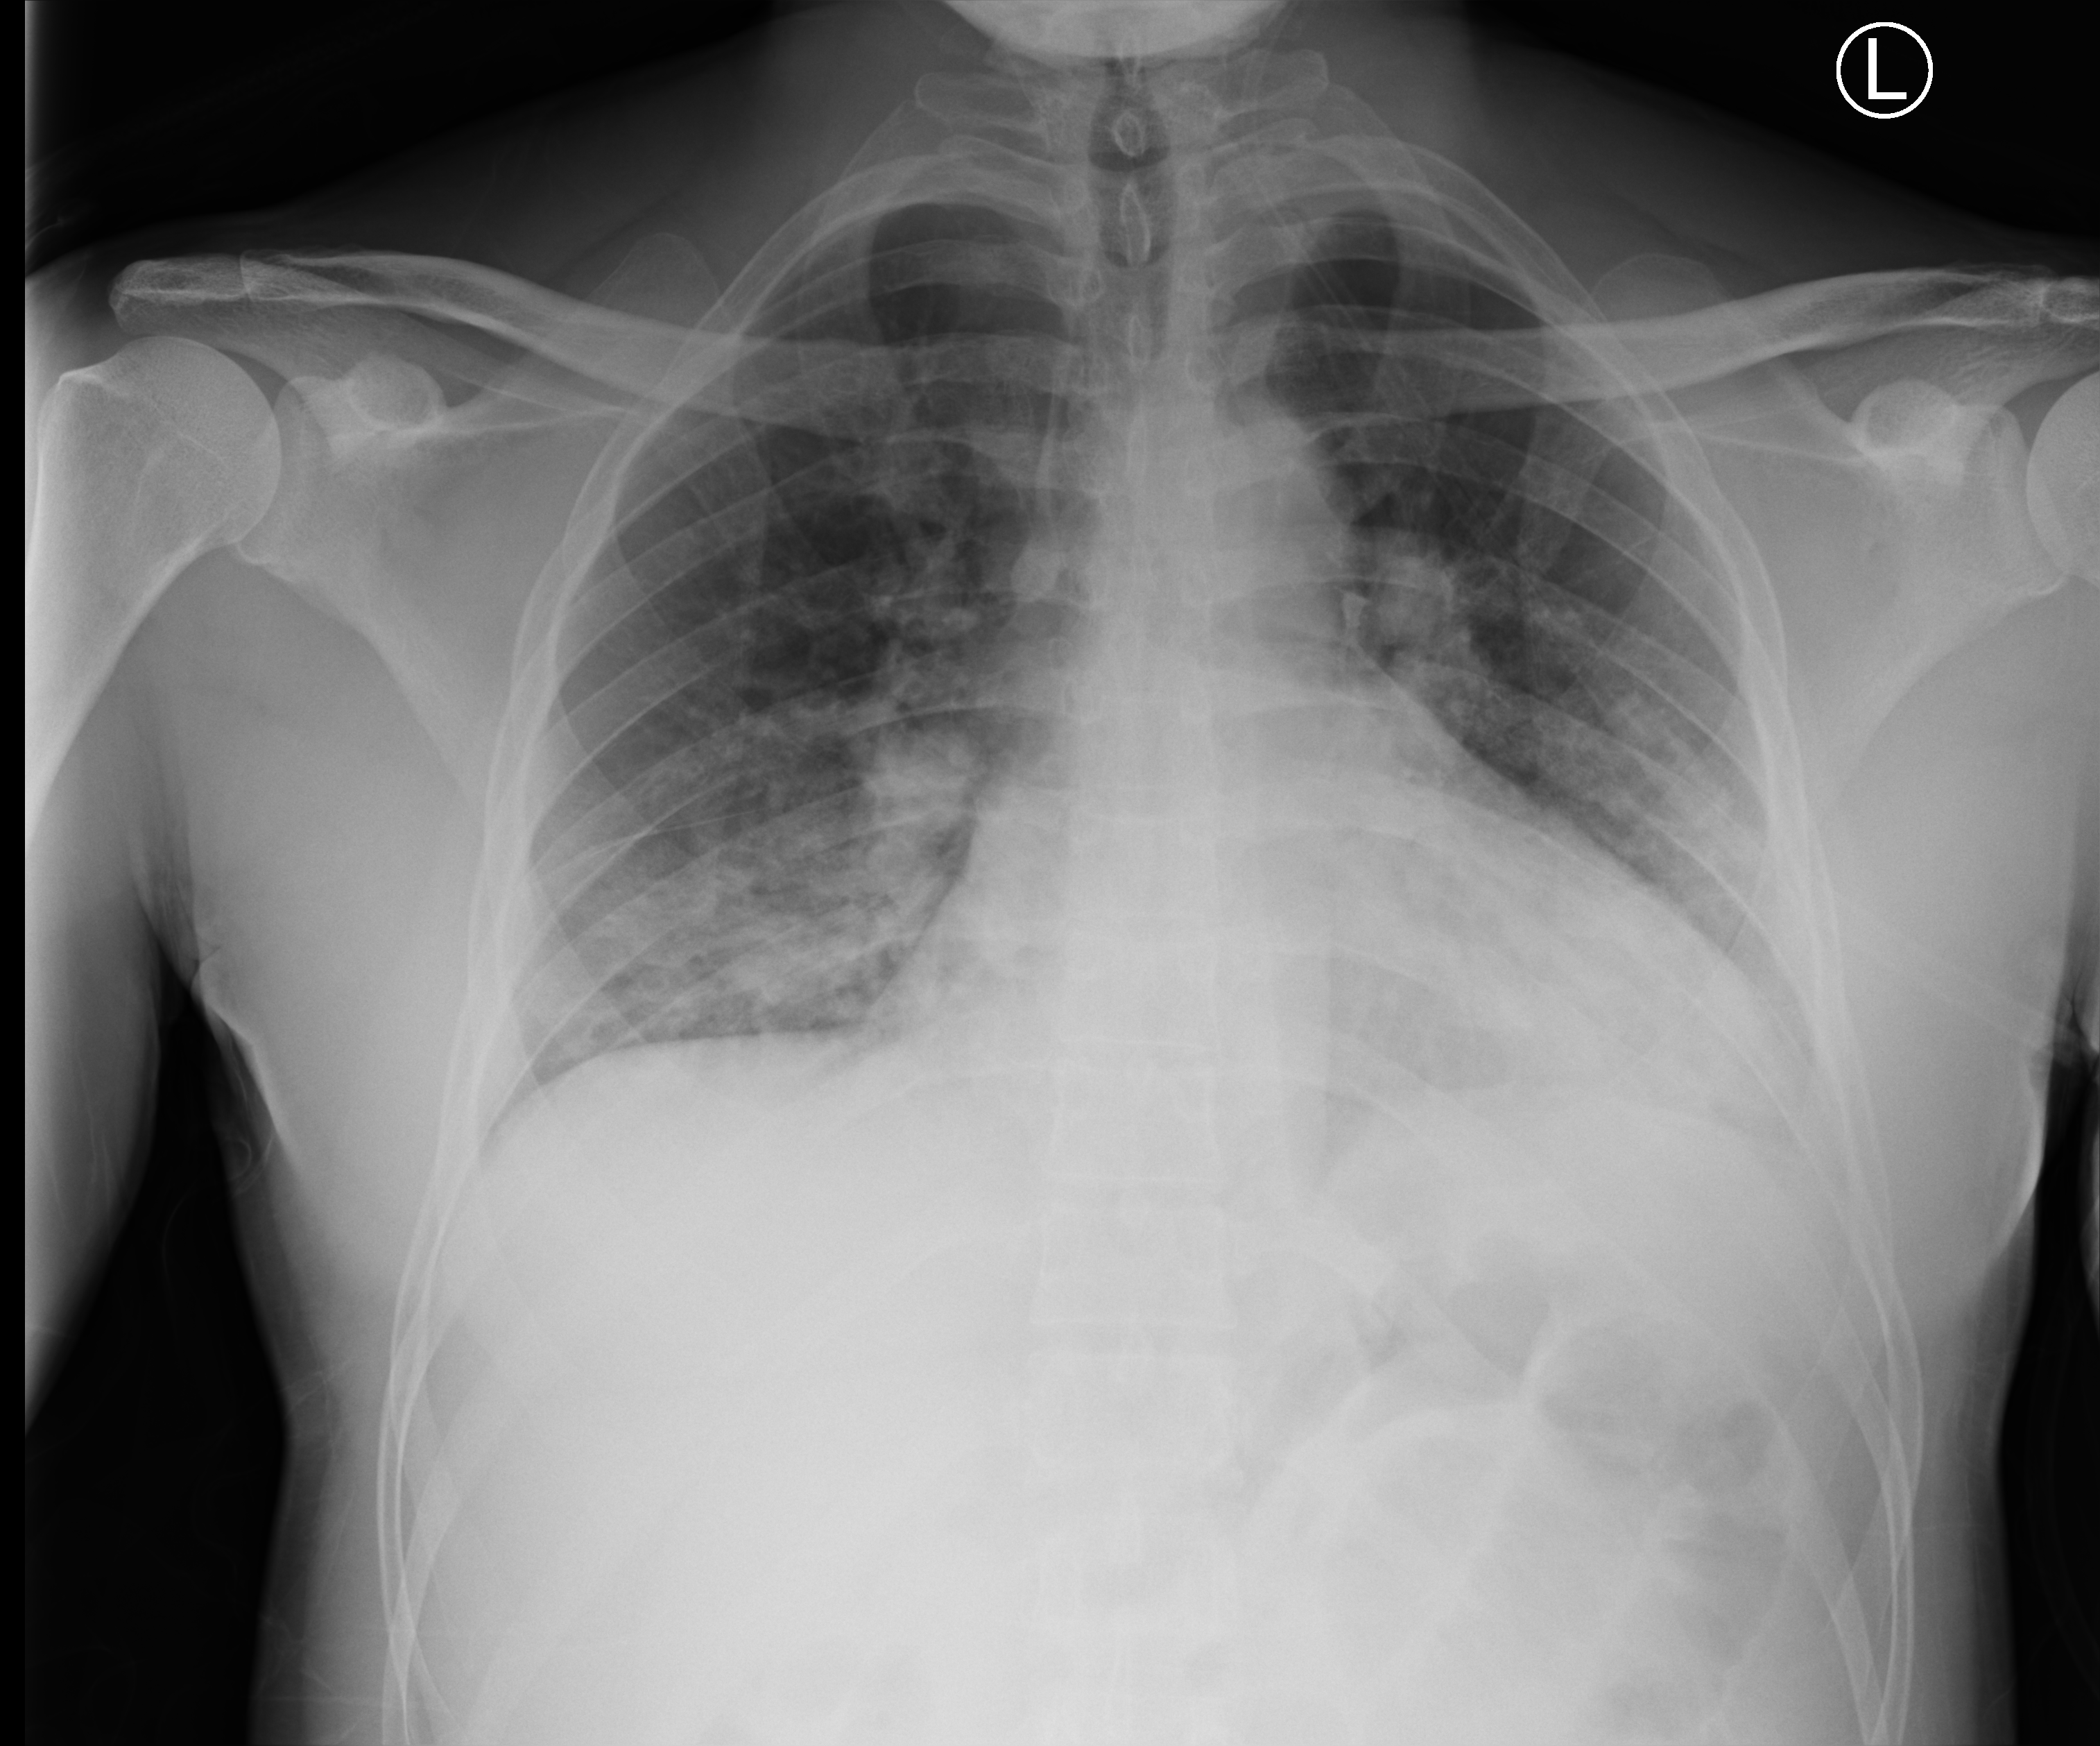
Bedside chest radiograph (computed radiography); anteroposterior (AP) projection. Male patient hospitalised with COVID-19, age 18–59 years.
Hospital-stay facts (about this admission, not read from this image; timing relative to this image not recorded): hypertension (admission record): no; mechanically ventilated during this hospital stay: no; COPD (admission record): no.